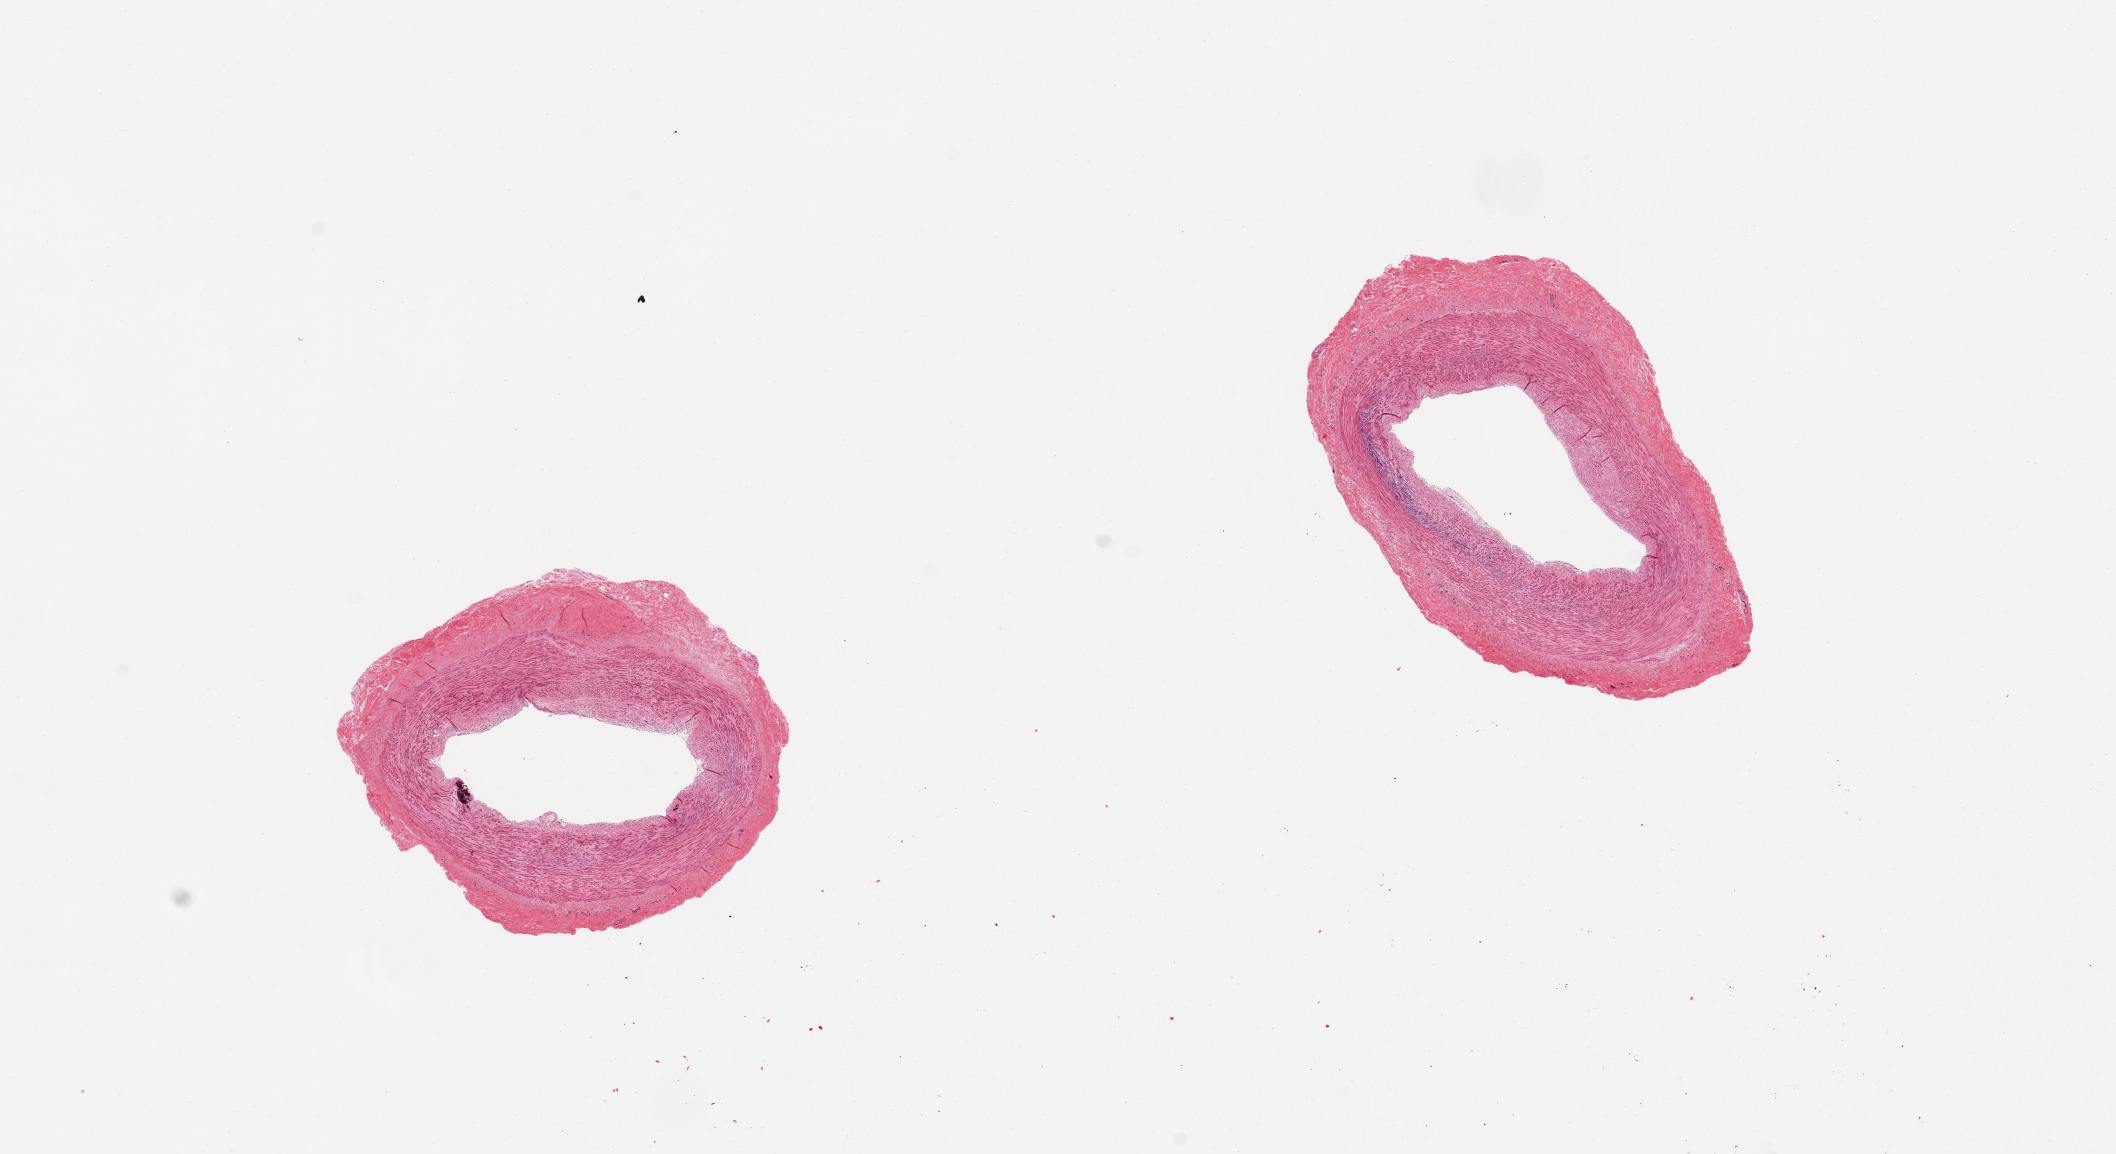
Hematoxylin and eosin (H&E) whole-slide image — whole scanned area (about 16.7 x 9.1 mm, slide scanned at 20x) shown as a low-resolution overview; PAXgene-fixed, paraffin-embedded tissue; sampled site (target tissue): tibial artery; tissue donor sample.
Pathologist's review note for this sample: 2 pieces; well trimmed.